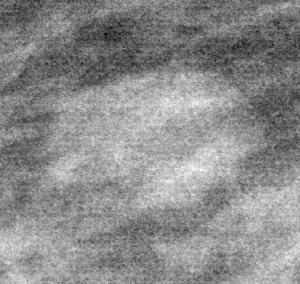
Crop from a digitized film mammogram around one marked abnormality, right breast, MLO view.
Finding: mass, shape round, margins circumscribed; BI-RADS assessment category 2; pathology (as recorded): benign.